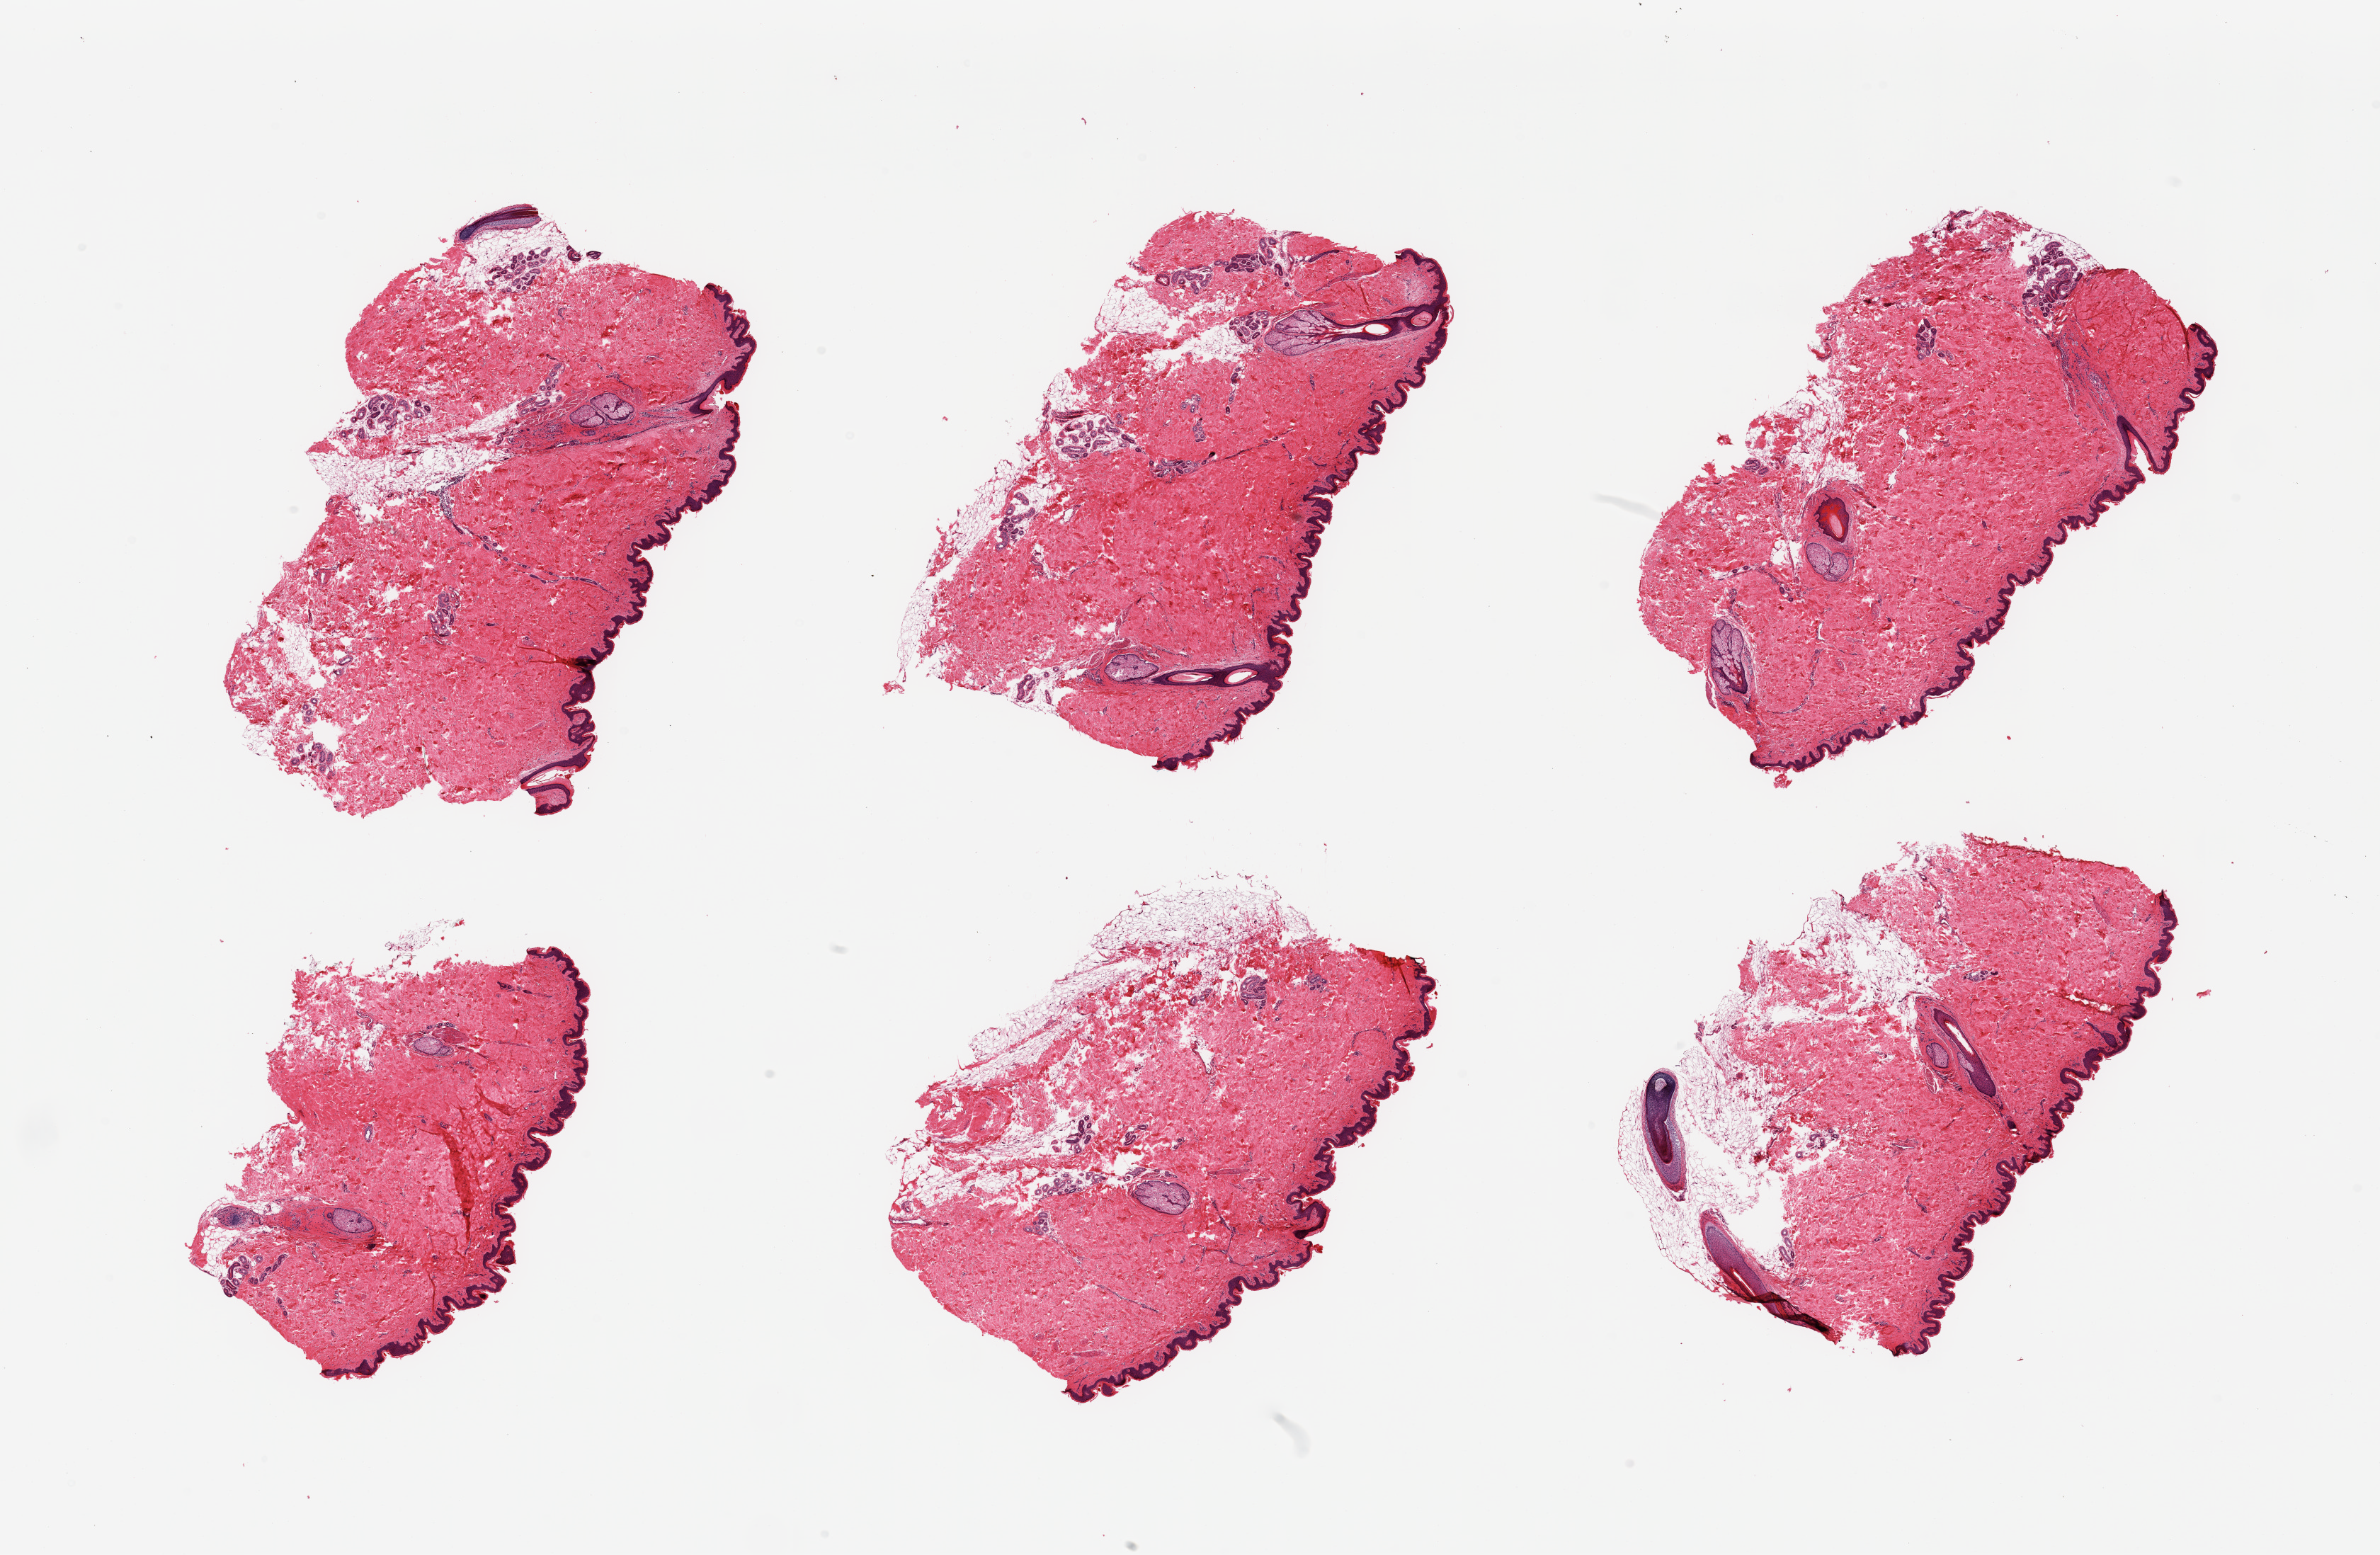
Digitized hematoxylin and eosin (H&E)-stained section — low-resolution overview of the scanned area, about 26.6 x 17.4 mm, PAXgene-fixed, paraffin-embedded tissue, section of skin of suprapubic region (target tissue), tissue donor sample. Donor sex: male.
Review note (as recorded): 6 pieces, trace adherent nubbins of dermal fat; squamous epithelium is ~50-60 microns.